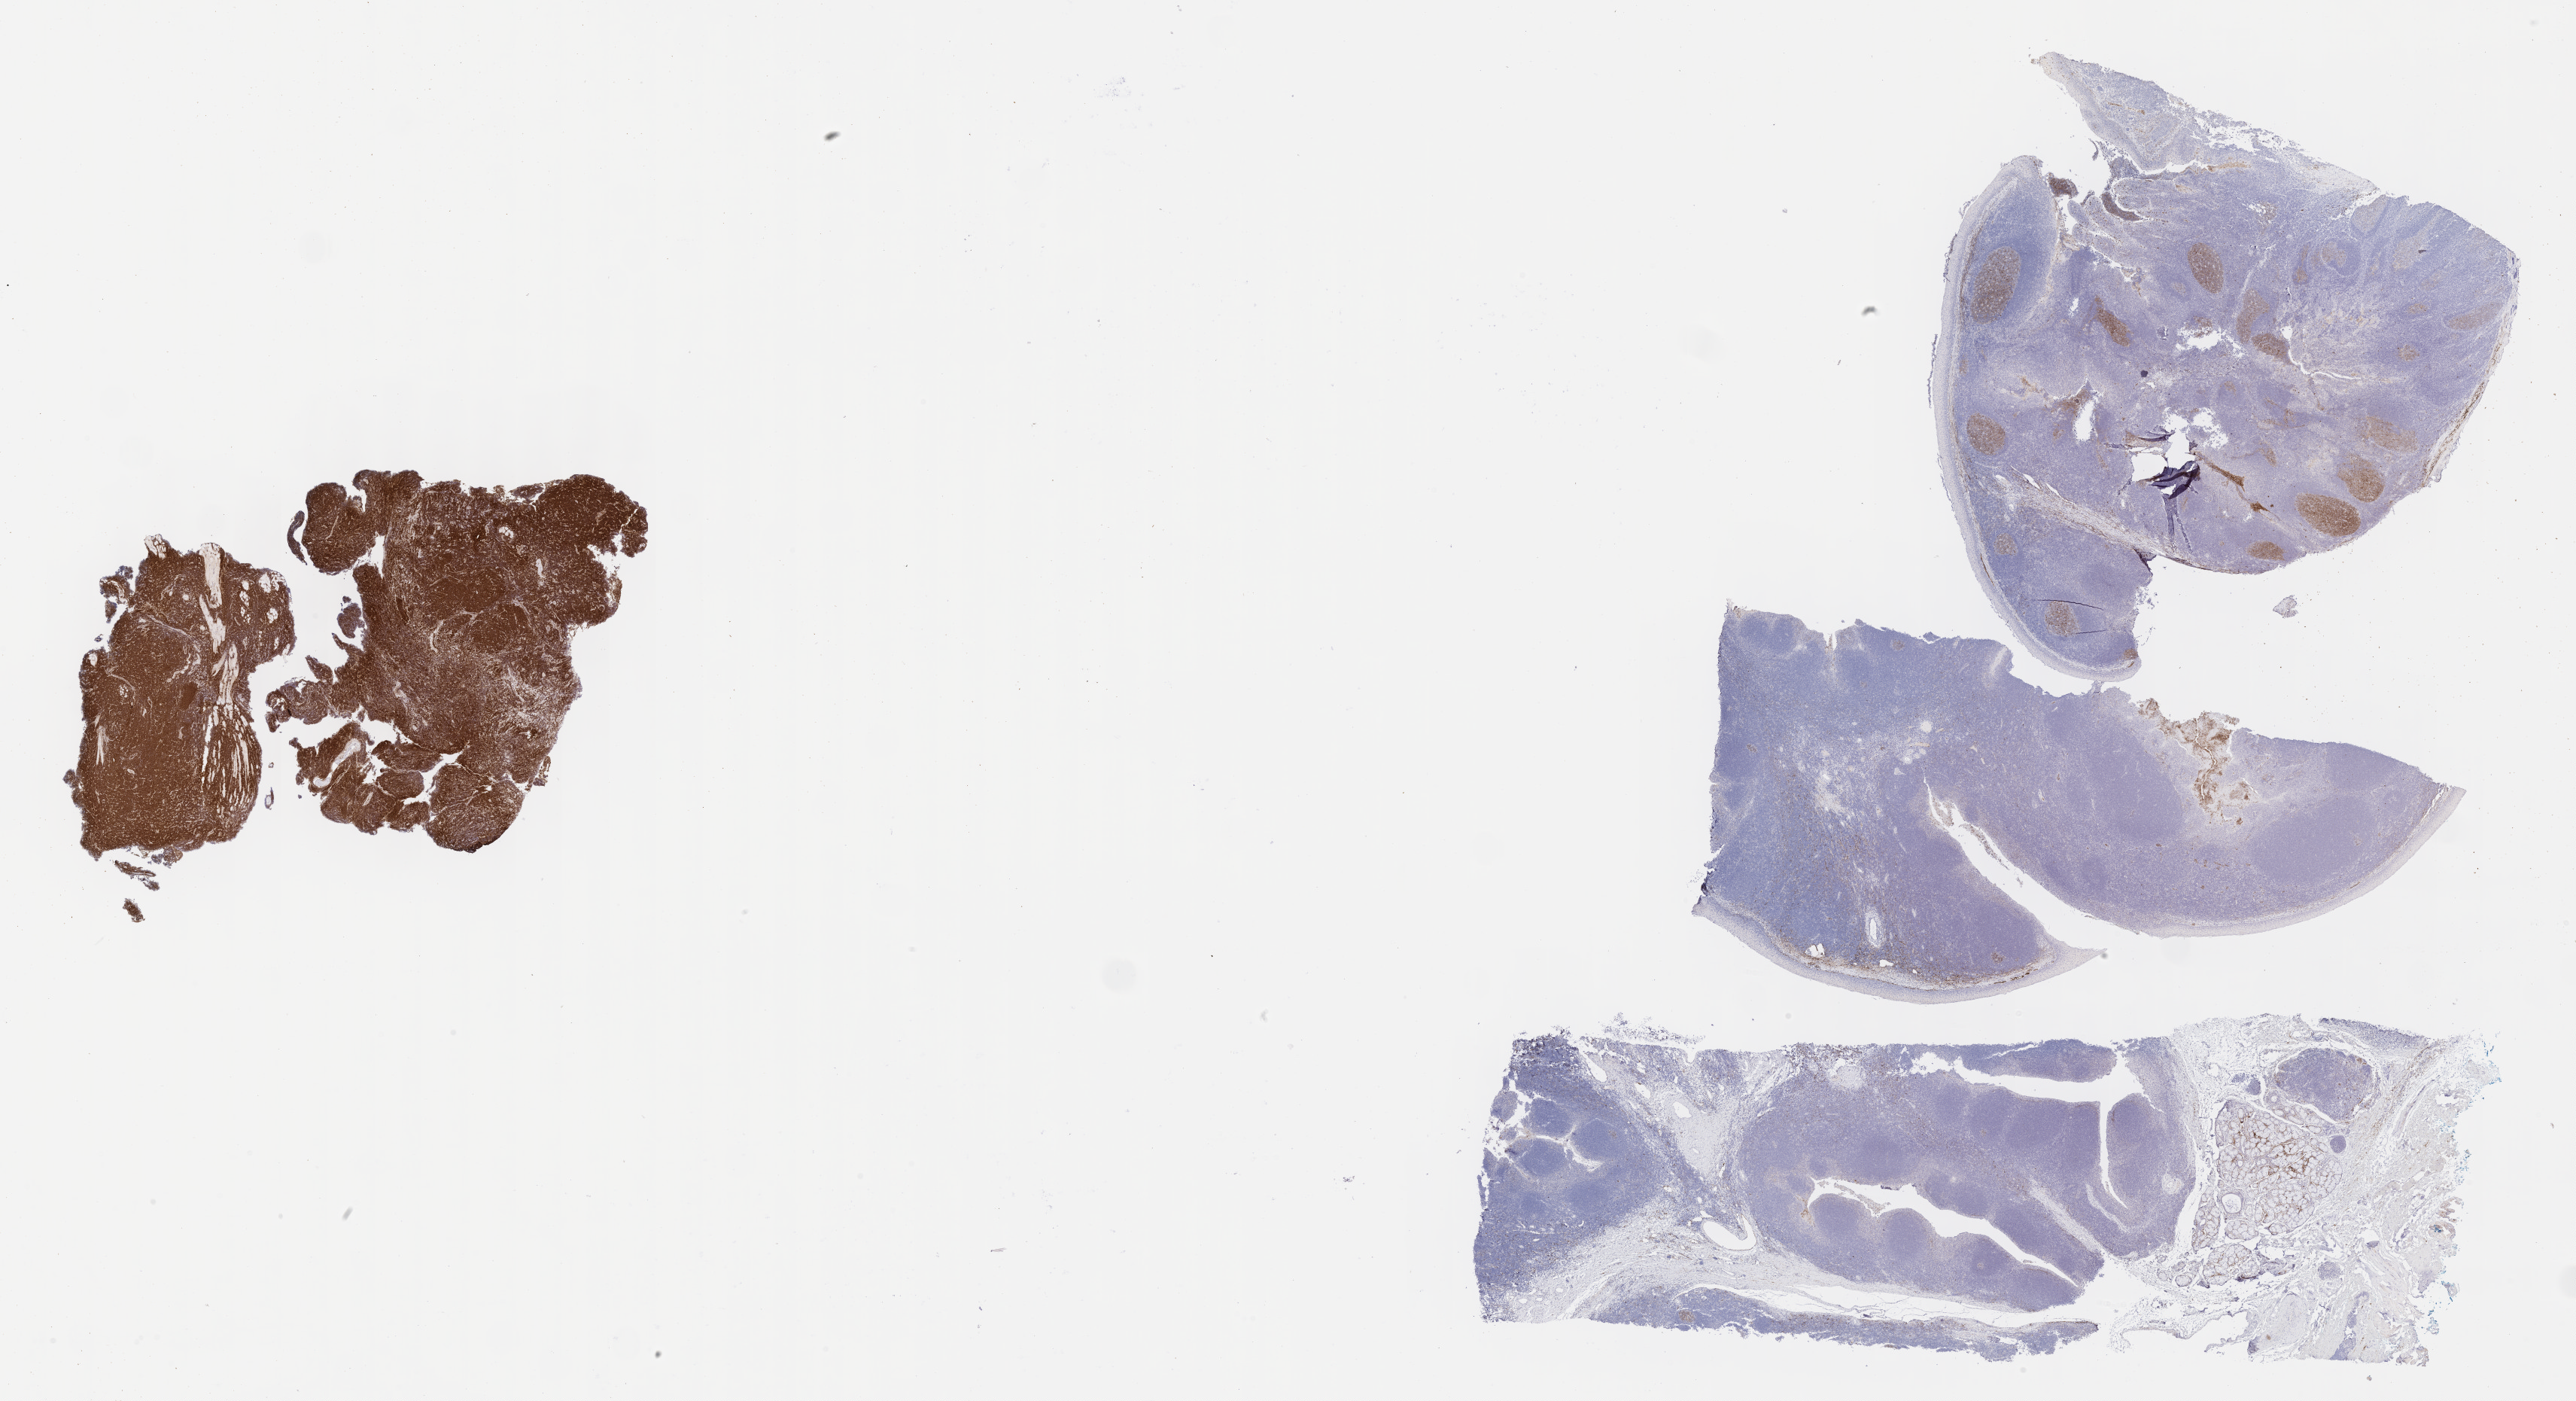
IHC for CD10, whole-slide image, whole scanned area (about 27.7 x 15.0 mm) shown as a low-resolution overview, specimen: tumor tissue, site: cranium. Male patient; age at initial diagnosis 8 years.
• diagnosis: Burkitt lymphoma, NOS